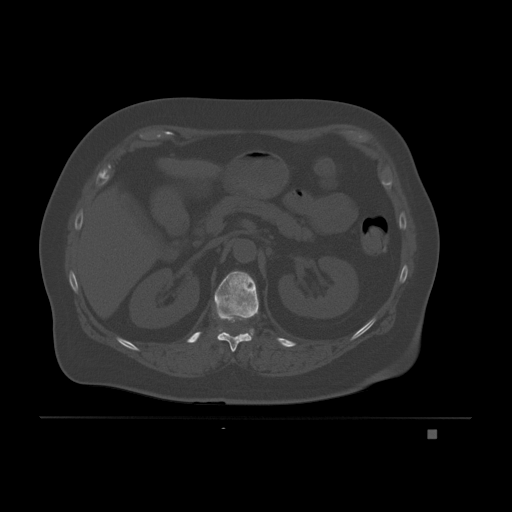
CT including the spine, one axial slice. Slice 86 of 221 in the series (ordered by position). Bone window (W 1800 / L 400 HU). 512 × 512 image matrix, field of view 474 × 474 mm. Female patient, age 63 years. Case-level facts recorded for this patient, not image findings: primary cancer: breast.
Annotated regions visible in this slice (semi-automatic segmentation, software-assisted and operator-edited):
- T11 vertebra: bounding box <213,313,253,352> (left, top, right, bottom; pixels)
- T12 vertebra: <214,271,259,320>